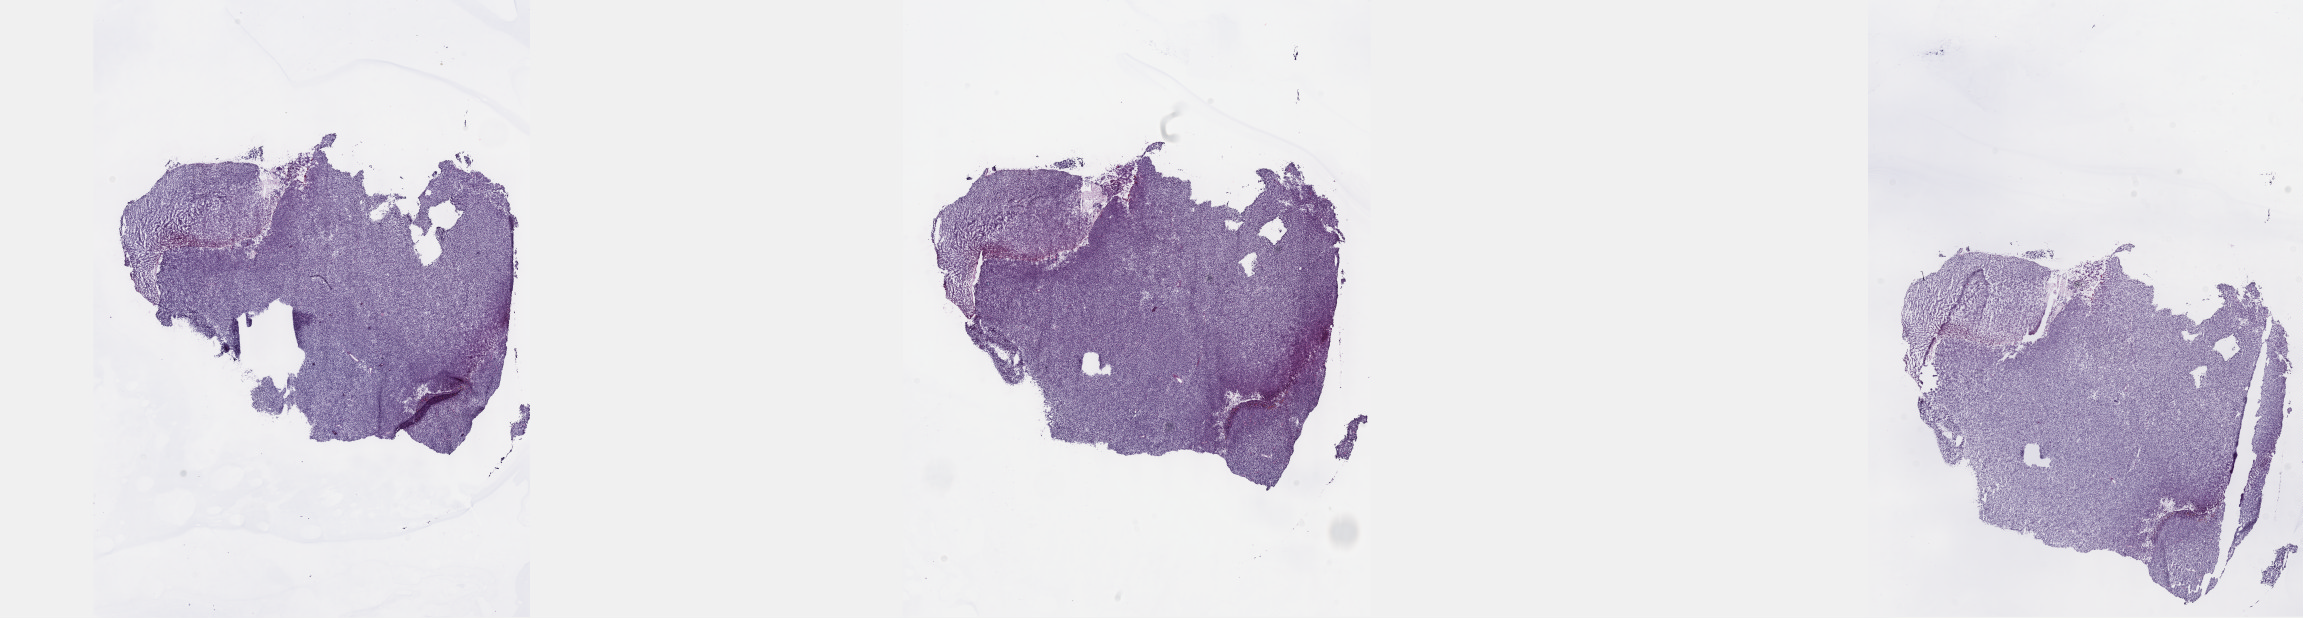
Whole-slide histology image, H&E, low-resolution overview of the scanned area, about 37.2 x 10.0 mm (acquisition: 40x scan). Frozen section from the top of the tissue portion. Brain, recurrent tumour sample. Female, age 24 years at initial diagnosis. Pathologist review of this section (percent, as recorded): tumour cells 85%, tumour nuclei 90%, normal cells 5%, stromal cells 5%, necrosis 5%. Infiltration values recorded for this section: lymphocyte infiltration 0%, monocyte infiltration 0%, neutrophil infiltration 0%.
- this section: recurrent tumour
- patient diagnosis: Oligodendroglioma, anaplastic (cerebrum)